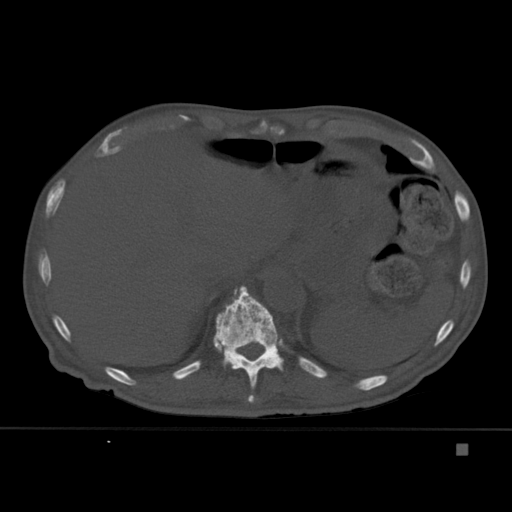
CT including the spine, one axial slice; slice 217 of 451 in the series (ordered by position); bone window (W 1800 / L 400 HU); 1.5 mm slice thickness; 512 × 512 image matrix, field of view 378 × 378 mm. Patient: male, 75 years. Case-level facts recorded for this patient, not image findings: primary cancer: prostate.
Outlined on this slice (semi-automatic segmentation, software-assisted and operator-edited):
- T11 vertebra: bounding box (x1, y1, x2, y2) in pixels: (213, 286, 284, 403)
- T12 vertebra: (242, 287, 280, 356)